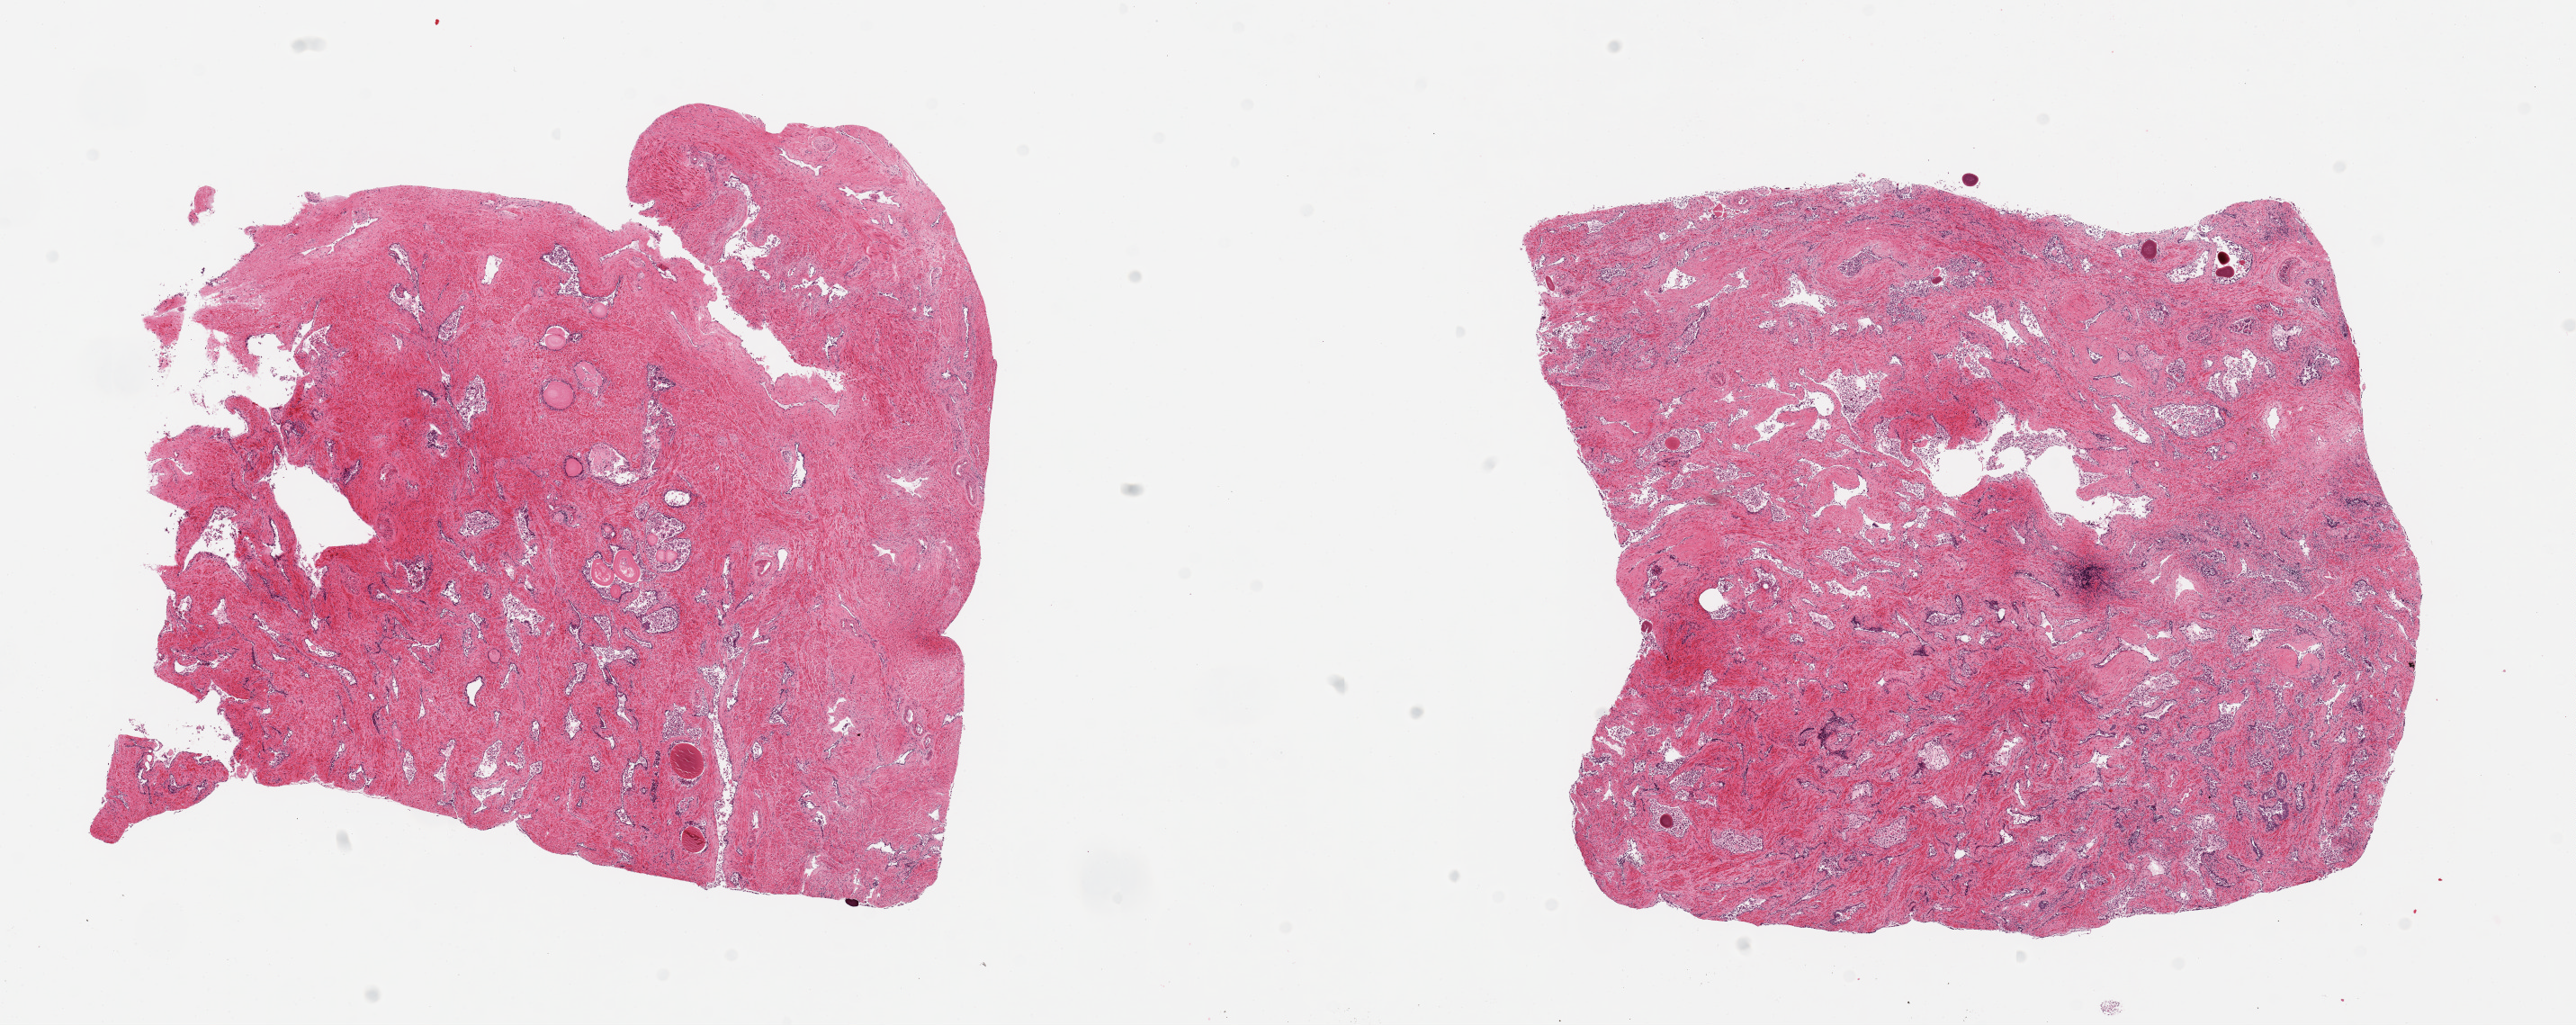
Haematoxylin and eosin whole-slide image, shown as a low-resolution overview of the whole scanned area (about 22.6 x 9.0 mm), PAXgene-fixed, paraffin-embedded tissue, sampled site (target tissue): prostate, donor tissue sample. Donor: male.
Reviewer comment on this tissue sample: 2 pieces, glandular hyperplastic pattern but epithelial elements with advanced autolysis.